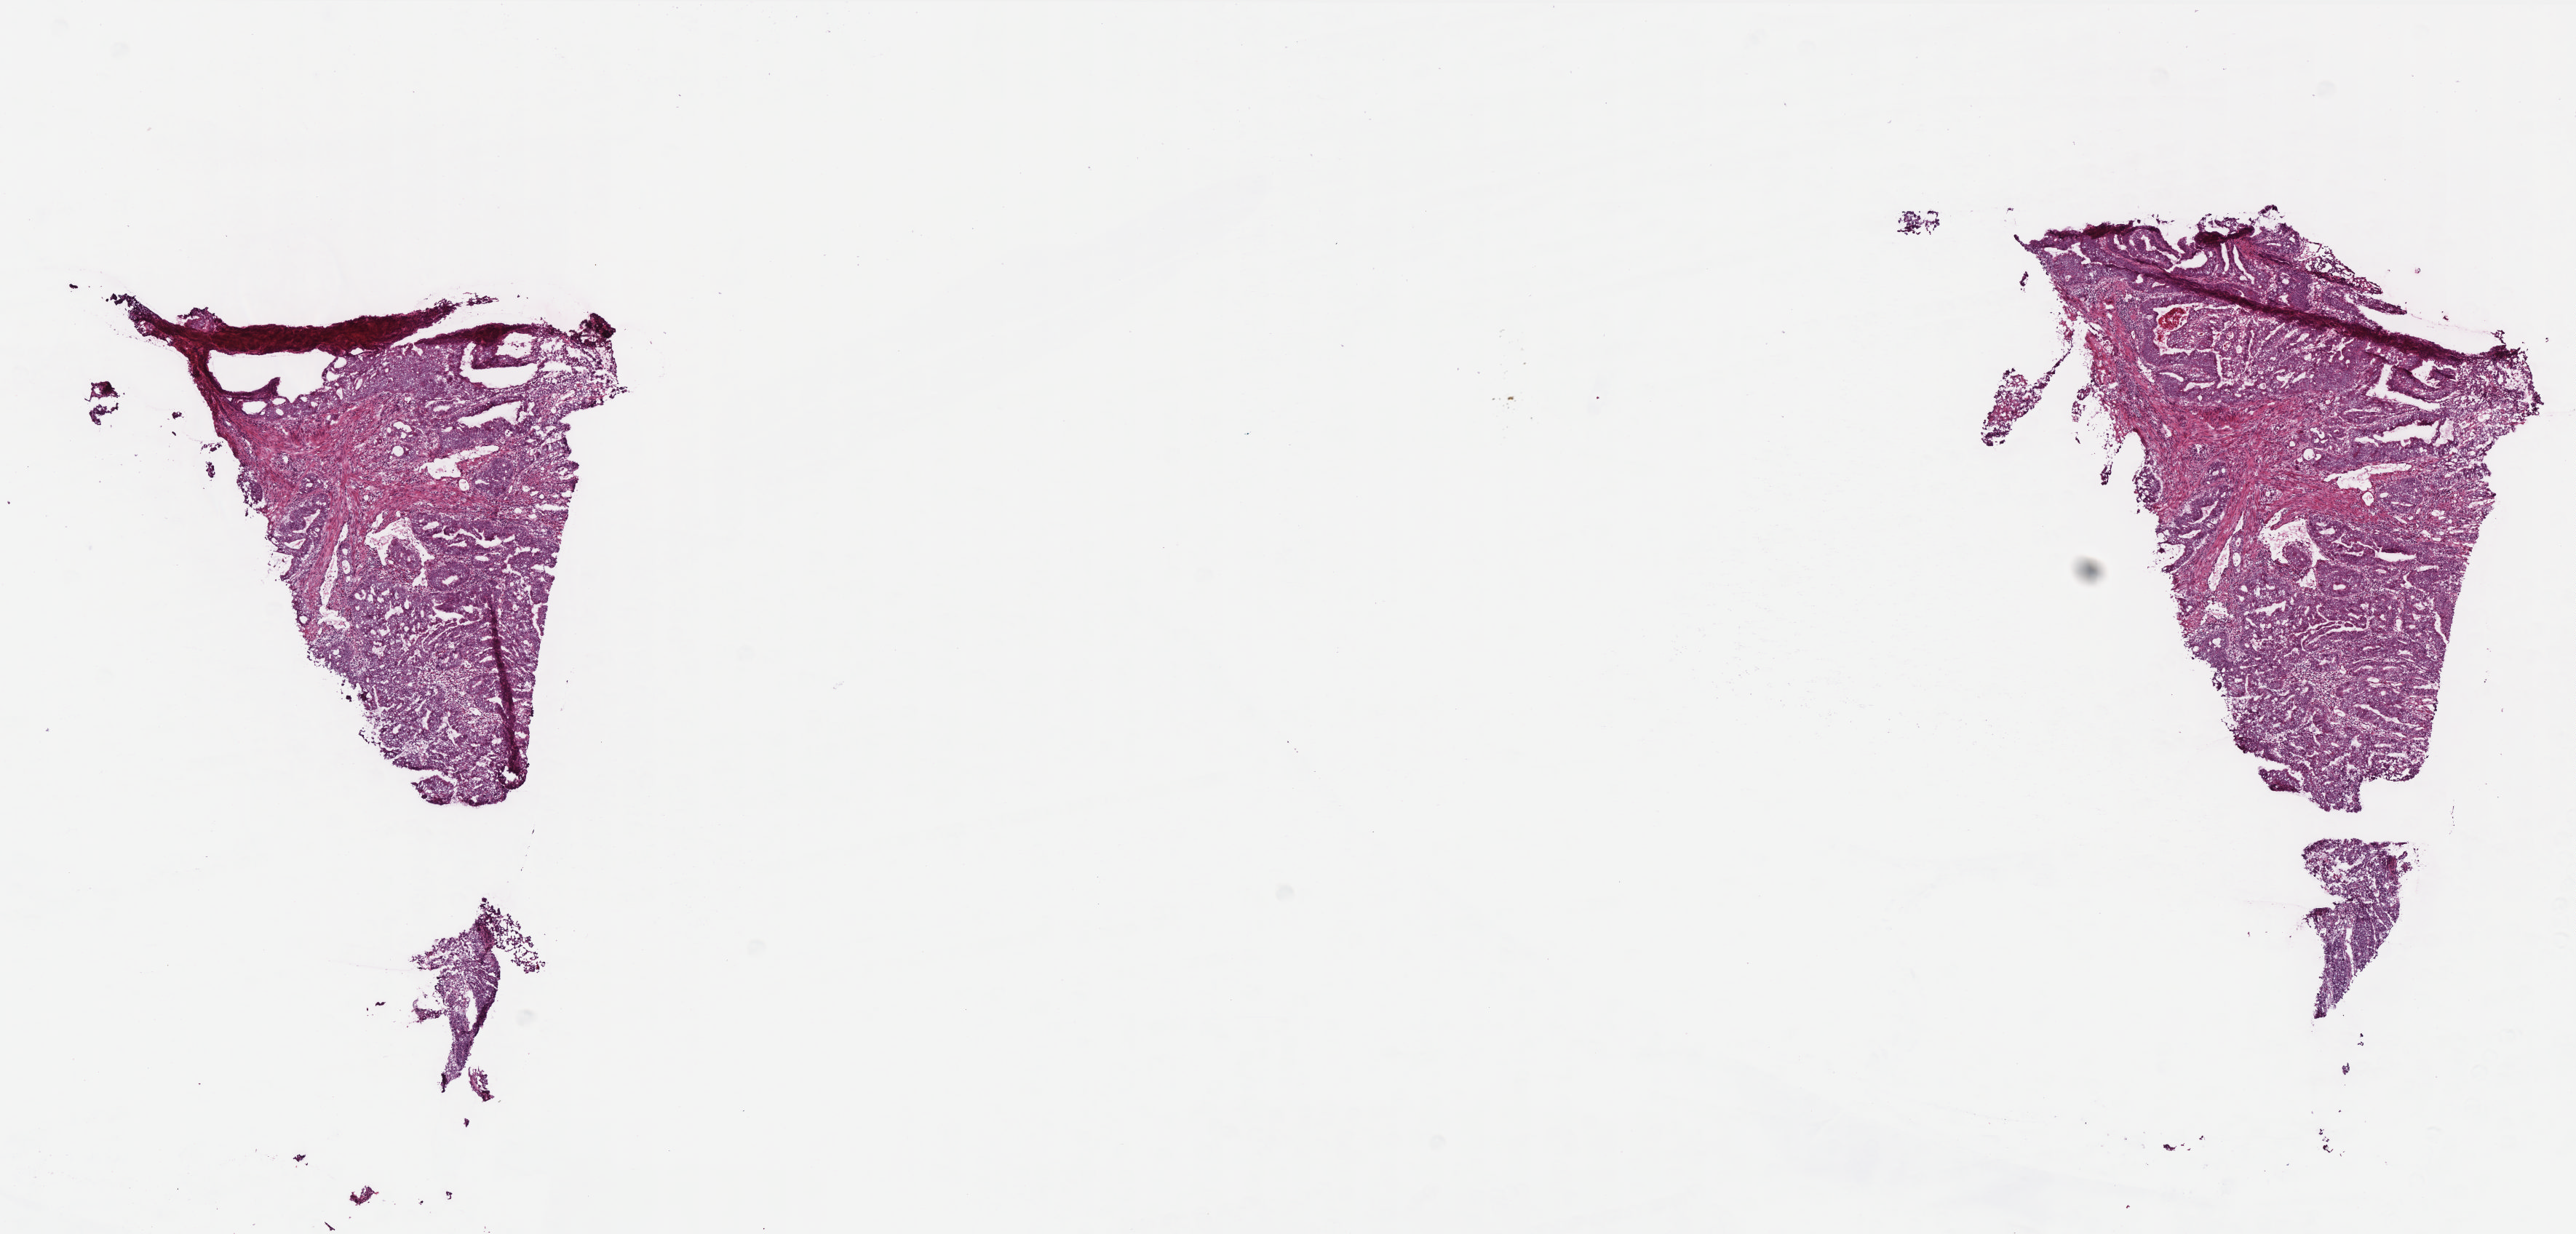
Digitized H&E-stained tissue section (whole slide) — shown as a low-resolution overview of the whole scanned area (about 14.2 x 6.8 mm, slide scanned at 40x), frozen section, primary tumour sample from the rectum. Female, age 49 years at initial diagnosis. Pathologist review of this section (percent, as recorded): tumour cells 85%, tumour nuclei 80%, normal cells 0%, stromal cells 14%, necrosis 1%. Infiltration values recorded for this section: lymphocyte infiltration 11%, monocyte infiltration 2%, neutrophil infiltration 1%.
* histologic diagnosis: Adenocarcinoma, NOS
* AJCC pathologic stage: IIIB (6th edition)
* lymph nodes positive (case pathology): 1 of 24 examined